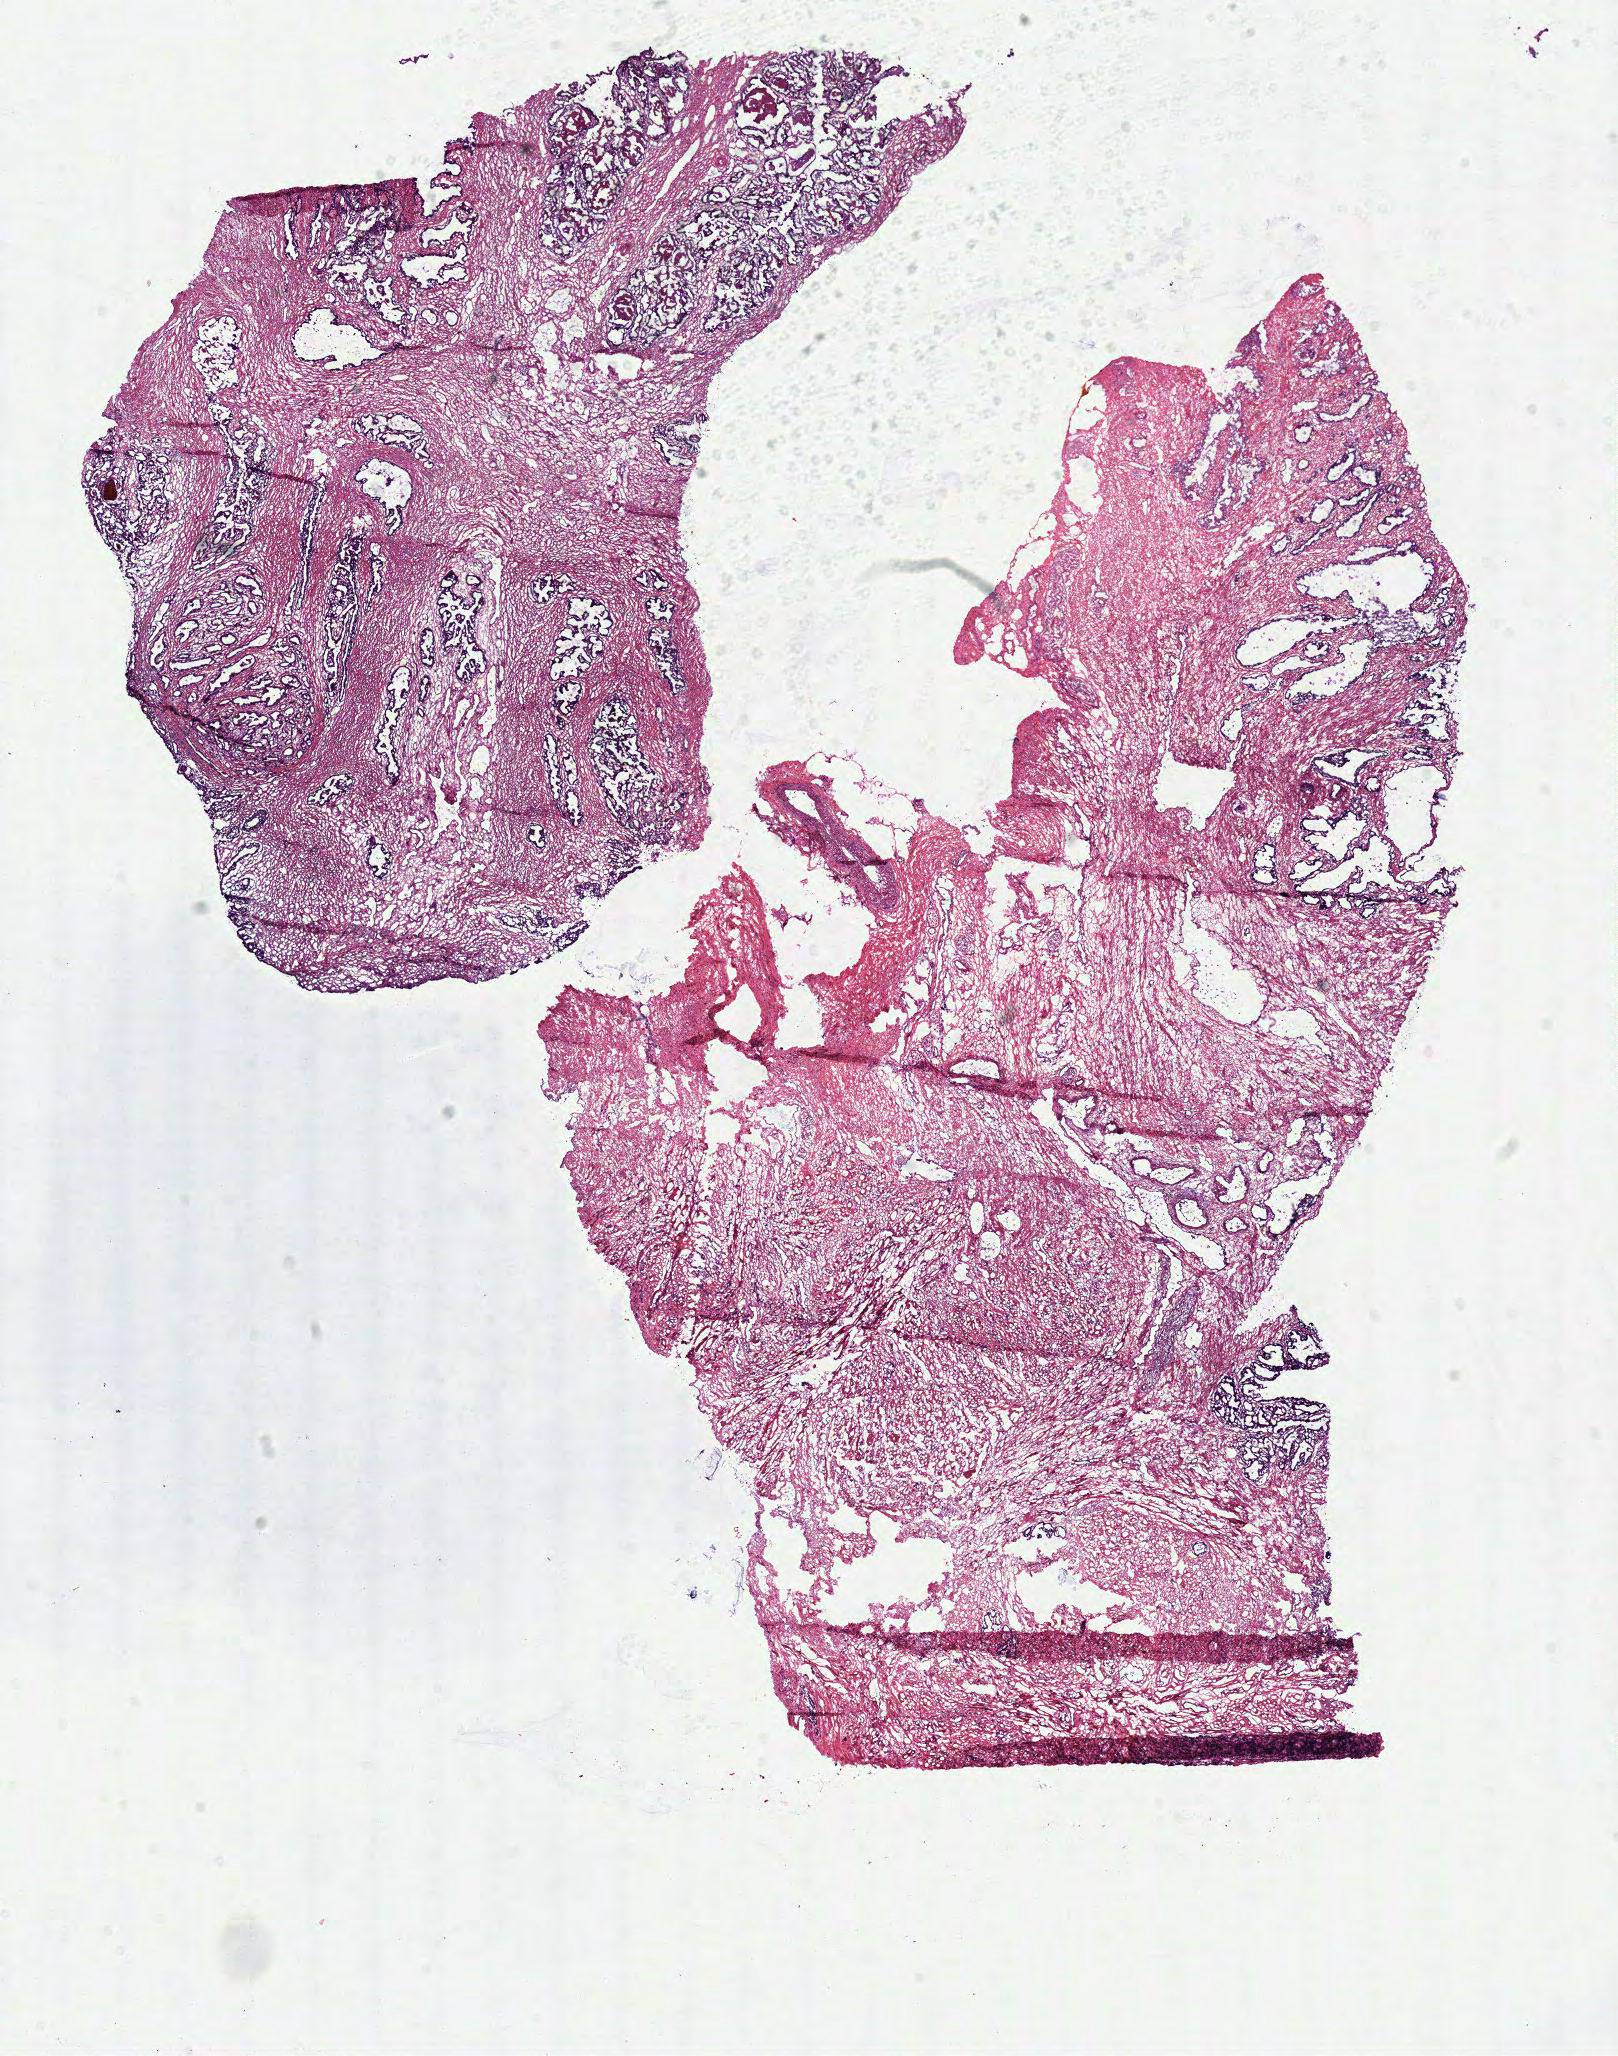
Whole-slide histology image, Hematoxylin and eosin (H&E) stained, a low-resolution overview of the entire scanned area, about 12.7 x 16.2 mm (slide scanned at 40x), frozen section from the top of the tissue portion, prostate, solid tissue normal (non-tumour tissue) sample. Male patient; age at initial diagnosis 60 years.
* this section: solid tissue normal (non-tumour) sample from the same patient
* patient diagnosis: Acinar cell carcinoma (prostate gland)